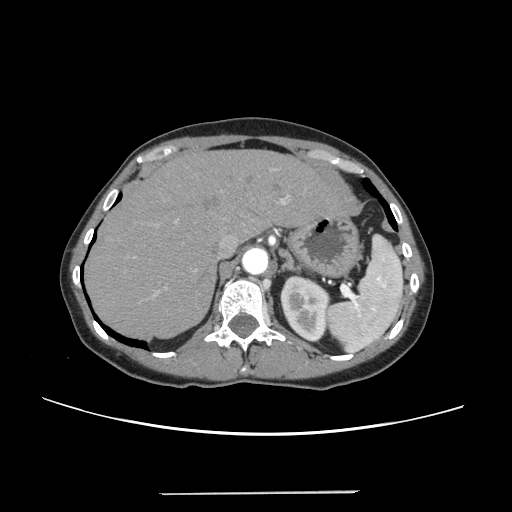
Contrast-enhanced abdominal CT, one axial slice. Position 182 of 240 along the scan axis. Intravenous contrast given. Soft-tissue window (W 400 / L 40 HU). 1.25 mm slice thickness. 512 × 512 image matrix, field of view 371 × 371 mm. Female patient, age 60 years. From the clinical record (not read from this slice): diagnosis: colorectal cancer liver metastases, imaged before liver resection; multiple liver metastases: no; largest metastasis: 1.5 cm.
Structures marked on this image (expert manual segmentation):
- hepatic veins: bounding box (x1, y1, x2, y2) in pixels: (220, 235, 238, 253)
- liver: (87, 150, 344, 338)
- planned liver remnant (the part of the liver to remain after resection): (87, 150, 343, 338)
- portal vein (with intrahepatic branches): (134, 196, 290, 295)